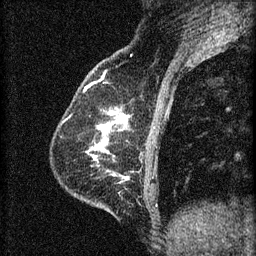
Breast MRI (dynamic contrast-enhanced), one sagittal slice; 3 images stored at this slice position (order not interpretable as contrast timing); 1.5 T; TE 4.2 ms, TR 8.2 ms; 2 mm slice thickness; 256 × 256 image matrix, field of view 180 × 180 mm. Patient: female, 59 years.
Structures marked on this image (semi-automatic segmentation, software-assisted and operator-edited):
- analysis volume of interest (the breast-tissue region the enhancement analysis was run in; not a lesion): box from (x=63, y=106) to (x=133, y=161) px
- tumour enhancement mask (voxels above the 70 % enhancement threshold inside the analysis volume of interest): (x=99, y=112)–(x=126, y=129)